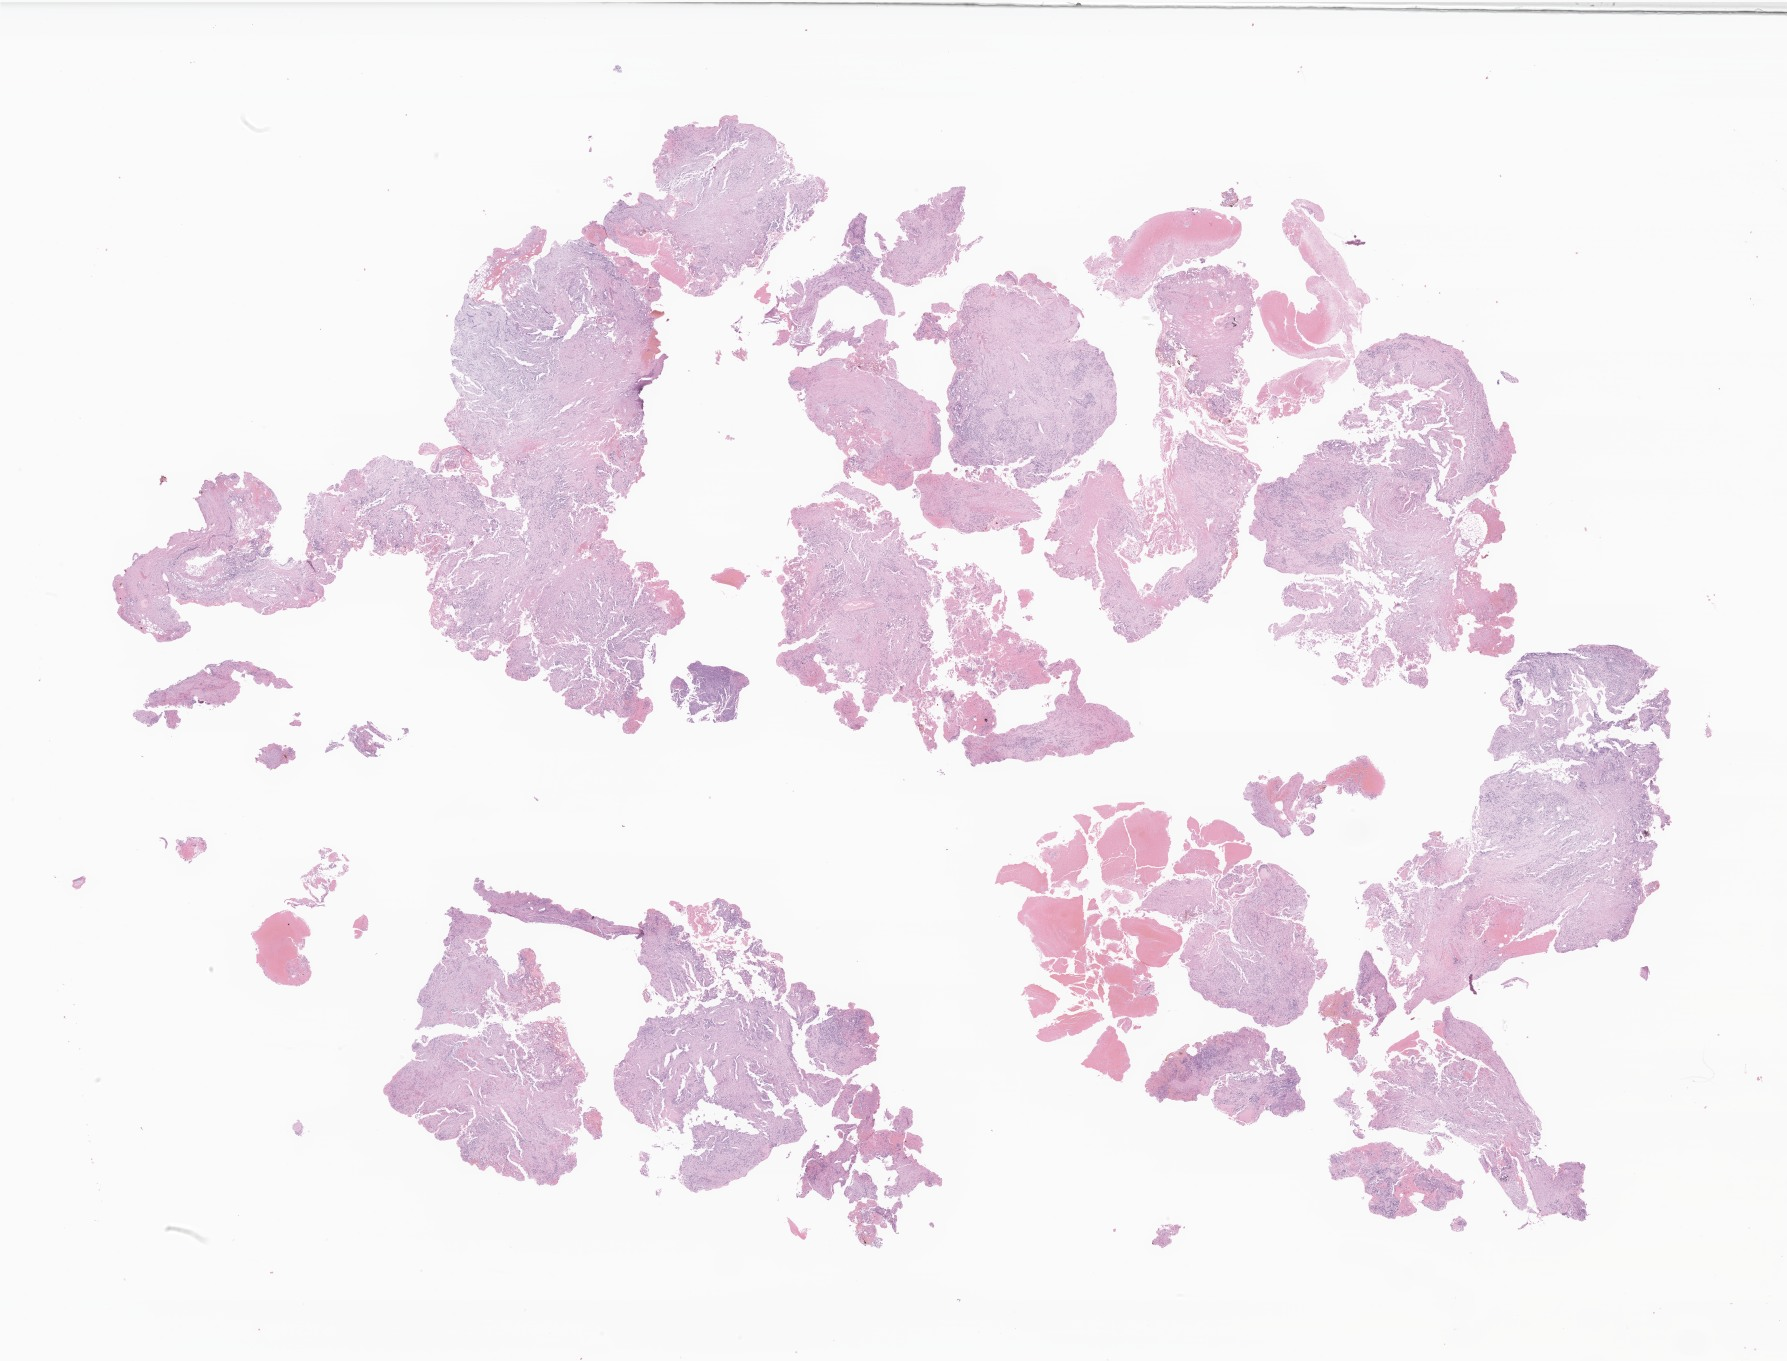
Digitized H&E-stained section of tumor tissue from the abdomen — a low-resolution overview of the entire scanned area, about 30.1 x 23.0 mm; formalin-fixed, paraffin-embedded (FFPE) tissue. Male patient, age 807 days (about 2.2 years).
Diagnosis (ICD-O-3 morphology term): Neuroblastoma, NOS.